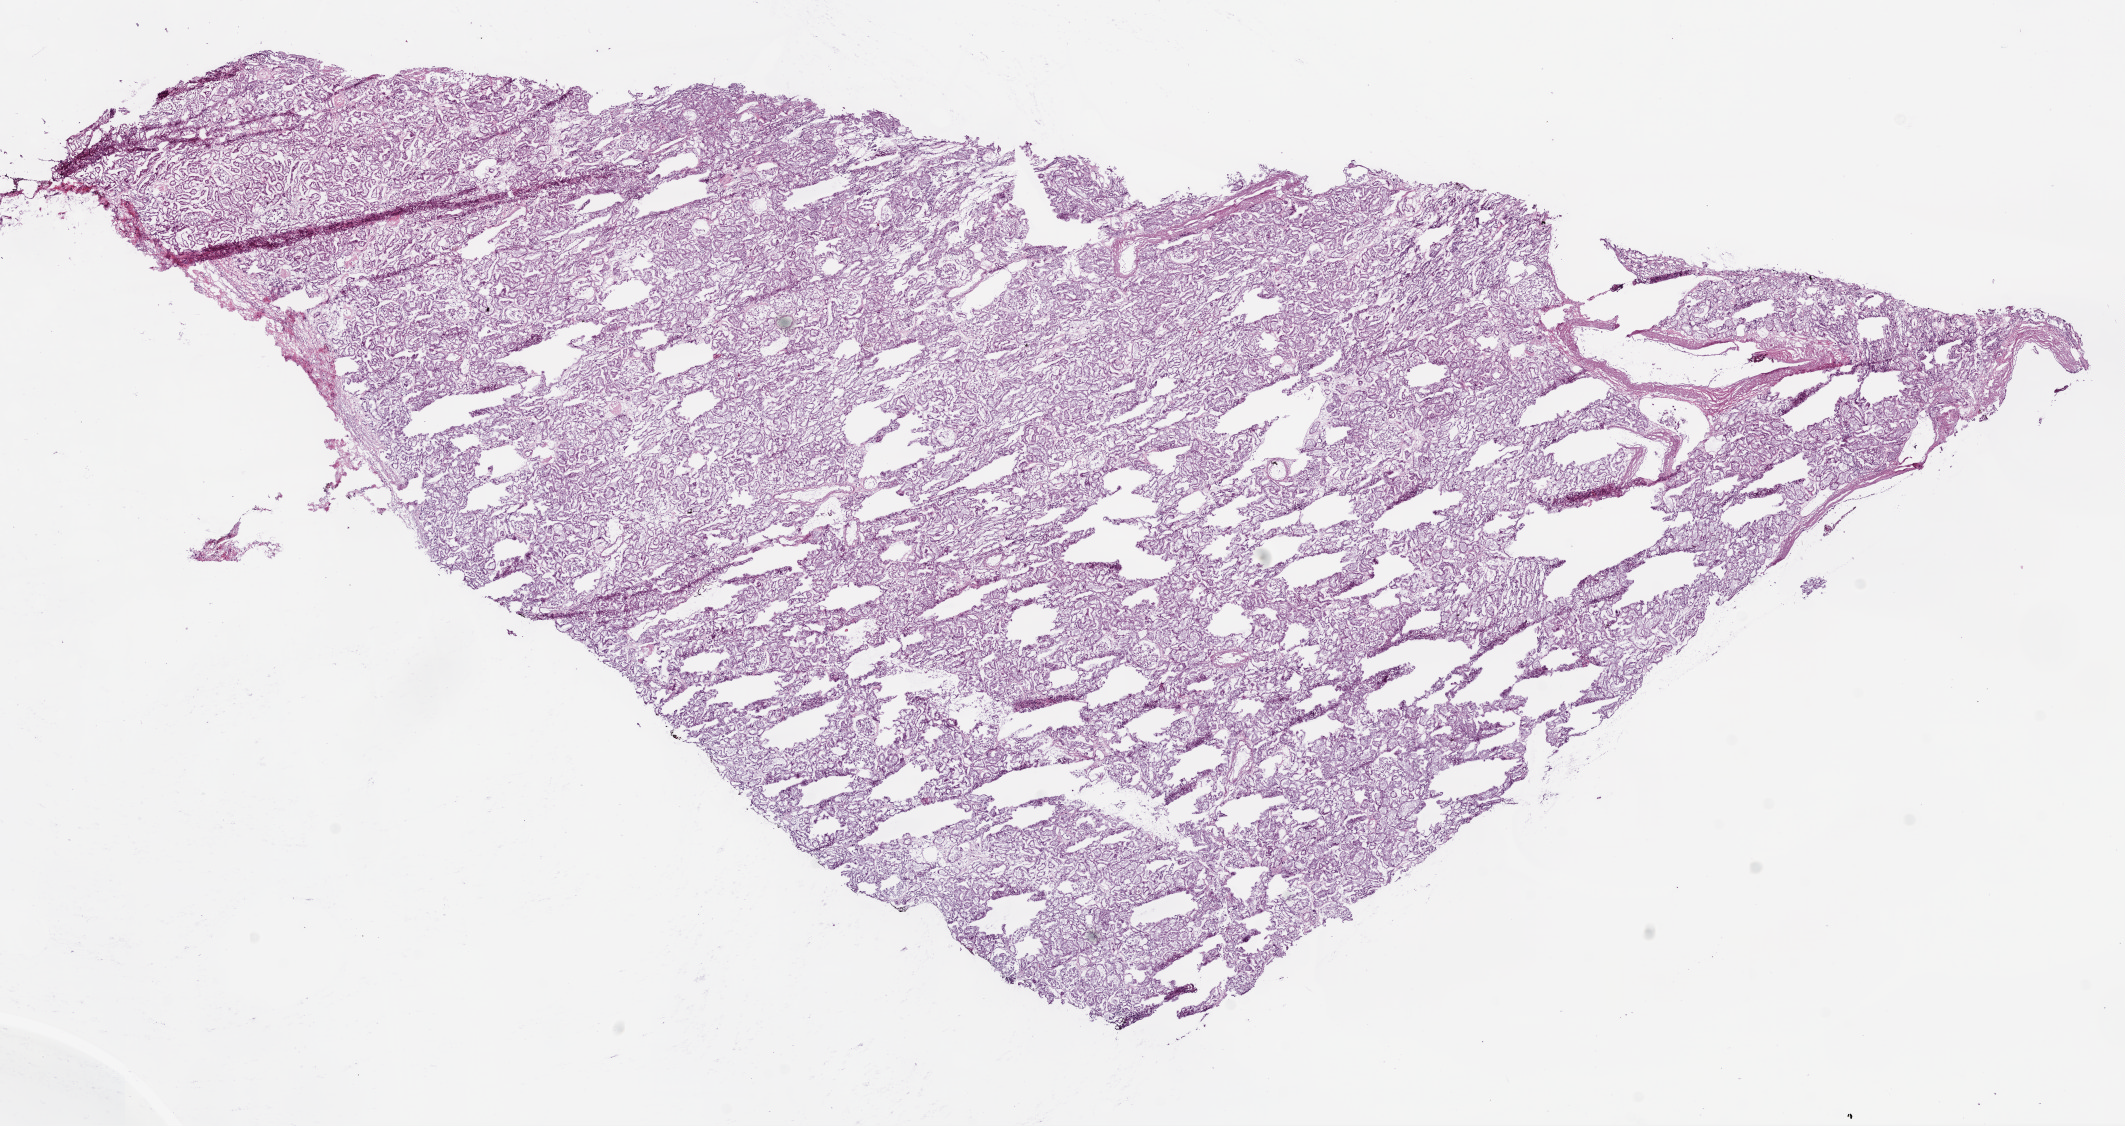
Digitized H&E tissue section (whole slide) — low-resolution overview of the scanned area, about 17.1 x 9.0 mm, frozen section from the bottom of the tissue portion, kidney, solid tissue normal (non-tumour tissue) sample. Male patient; age at initial diagnosis 62 years.
This section: solid tissue normal sample (biorepository sample class). Patient diagnosis: Clear cell adenocarcinoma, NOS.